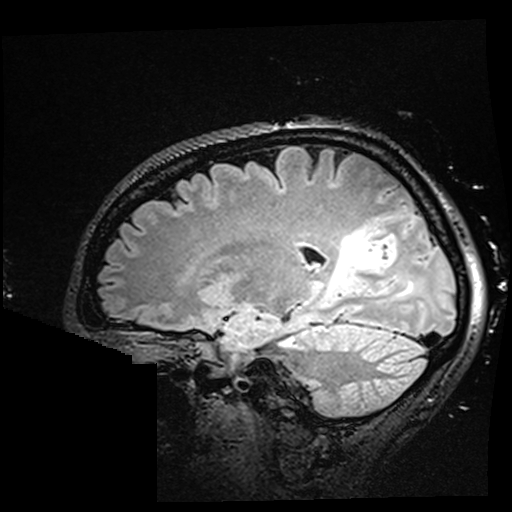
Brain MRI from a brain-tumour surgery series, one sagittal slice. Slice 111 of 176 in the series (ordered by position). T2 FLAIR. 512 × 512 image matrix, field of view 250 × 250 mm. From the clinical record (not read from this slice): histopathology: Oligodendroglioma; WHO grade: 2; IDH mutation: yes; tumour location: Right Parietal.
Outlined on this slice (outlined manually by an expert reader):
- residual tumour: bounding box <326,230,387,294> (left, top, right, bottom; pixels)